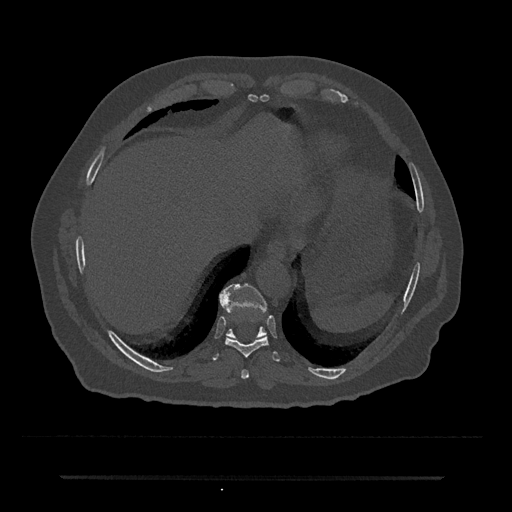
CT including the spine, one axial slice; slice 265 of 797 in the series (ordered by position); reconstruction kernel Br40s/3; bone window (W 1800 / L 400 HU); 0.5 mm slice thickness; 512 × 512 image matrix, field of view 437 × 437 mm. Patient: male, 69 years. From the clinical record (not read from this slice): primary cancer: prostate.
Annotated regions visible in this slice (semi-automatically segmented with operator editing):
- T10 vertebra: bounding box [x1, y1, x2, y2] px = [219, 283, 267, 339]
- T8 vertebra: [241, 369, 249, 379]
- T9 vertebra: [212, 291, 280, 361]